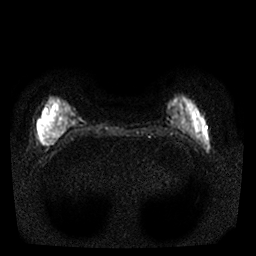
Breast MRI, one axial slice. Slice 3 of 25 in the series (ordered by position). Diffusion-weighted series; image 2 of 4 stored at this slice position (different b-values; order by instance number). 1.5 T. 256 × 256 image matrix. Female patient.
Annotated regions visible in this slice (manually delineated by an expert):
- tumour on diffusion-weighted imaging: bounding box (x1, y1, x2, y2) in pixels: (39, 134, 46, 145)